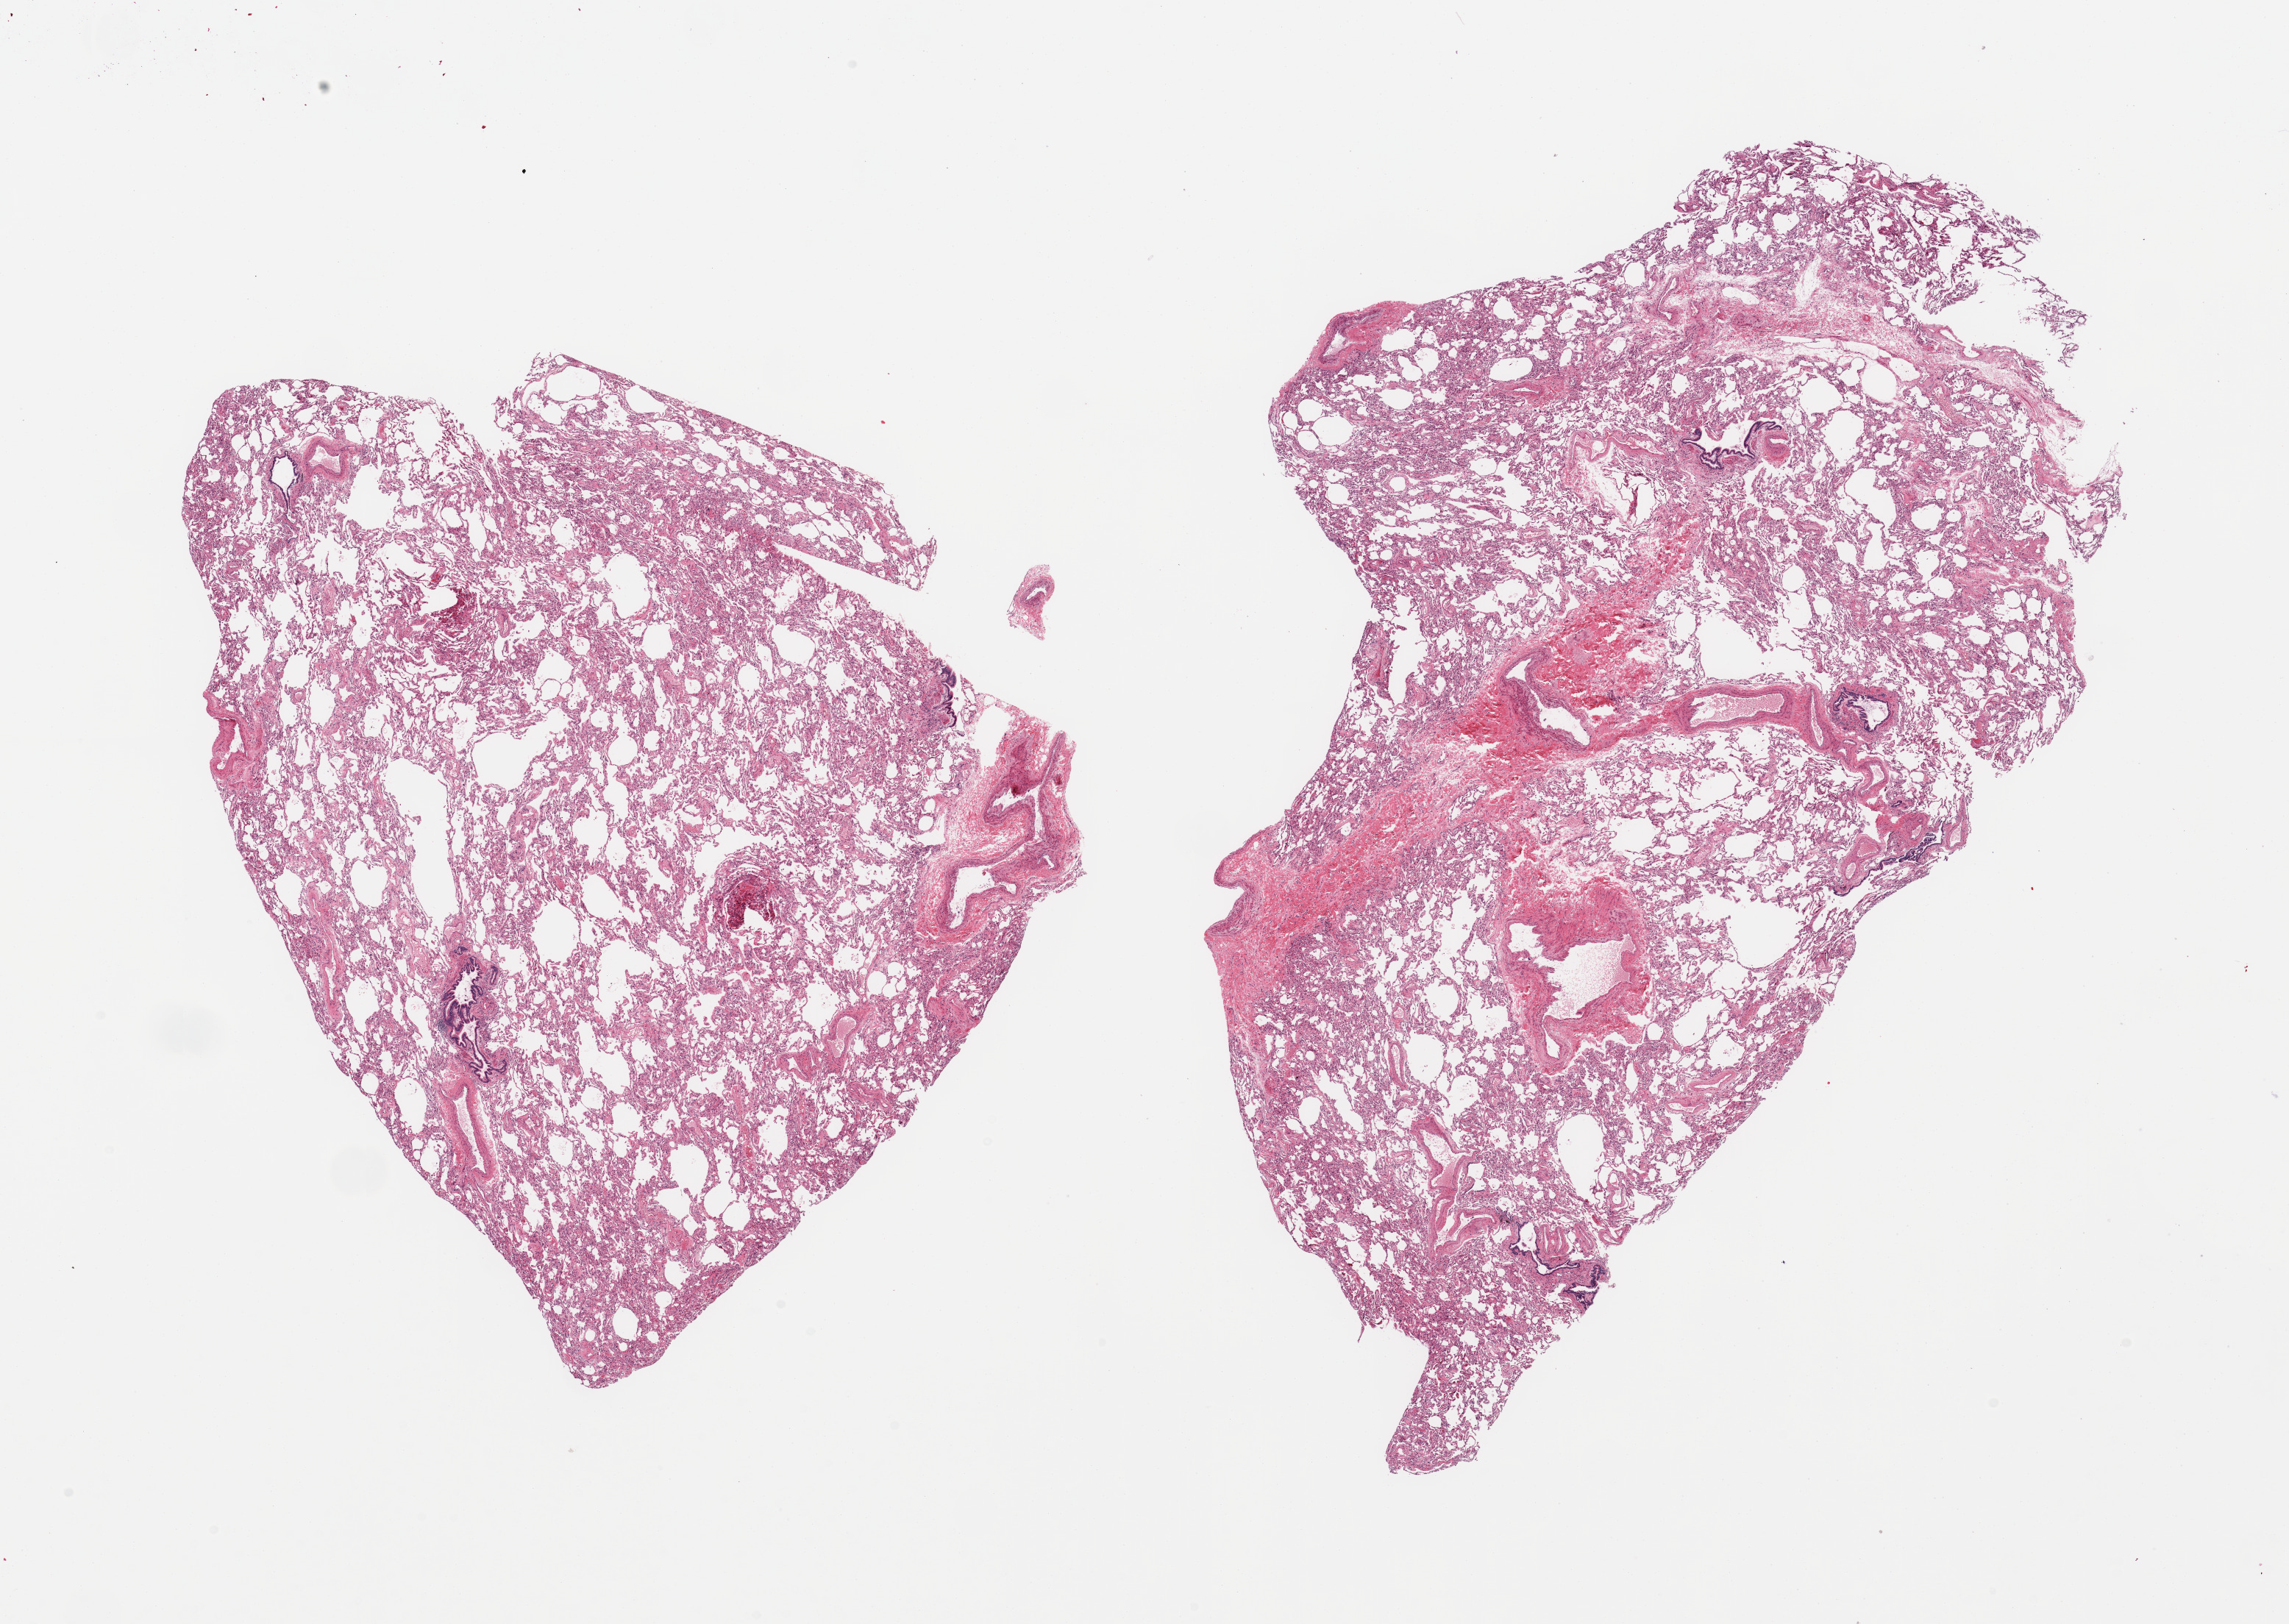
Whole-slide image, hematoxylin and eosin (H&E) stain, brightfield, shown as a low-resolution overview of the whole scanned area (about 24.6 x 17.5 mm, from a 20x scan), PAXgene-fixed, paraffin-embedded tissue, sampled site (target tissue): lung, tissue donor sample. Donor sex: female.
Review note (as recorded): 2 pieces; well preserved without lesions.